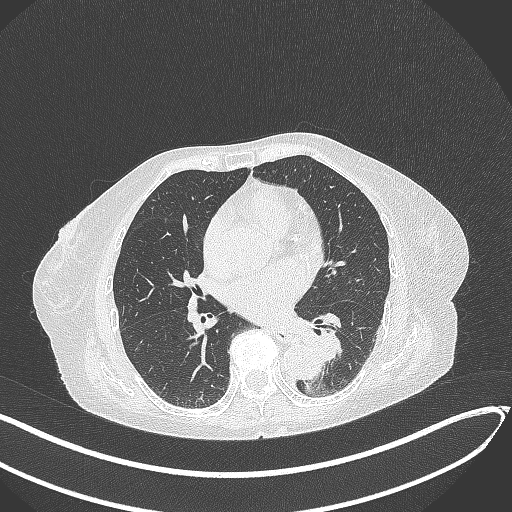
Chest CT, one axial slice. Position 117 of 324 along the scan axis. 120 kVp. Lung window (W 1500 / L -600 HU). 512 × 512 image matrix, field of view 400 × 400 mm. Female patient, age 82 years. From the clinical record (not read from this slice): clinical TNM (as recorded): T1b N0 M1.
Structures marked on this image (rectangle marked by the reading radiologist):
- lung tumour (recorded histology: adenocarcinoma): bounding box (x1, y1, x2, y2) in pixels: (298, 322, 351, 368)